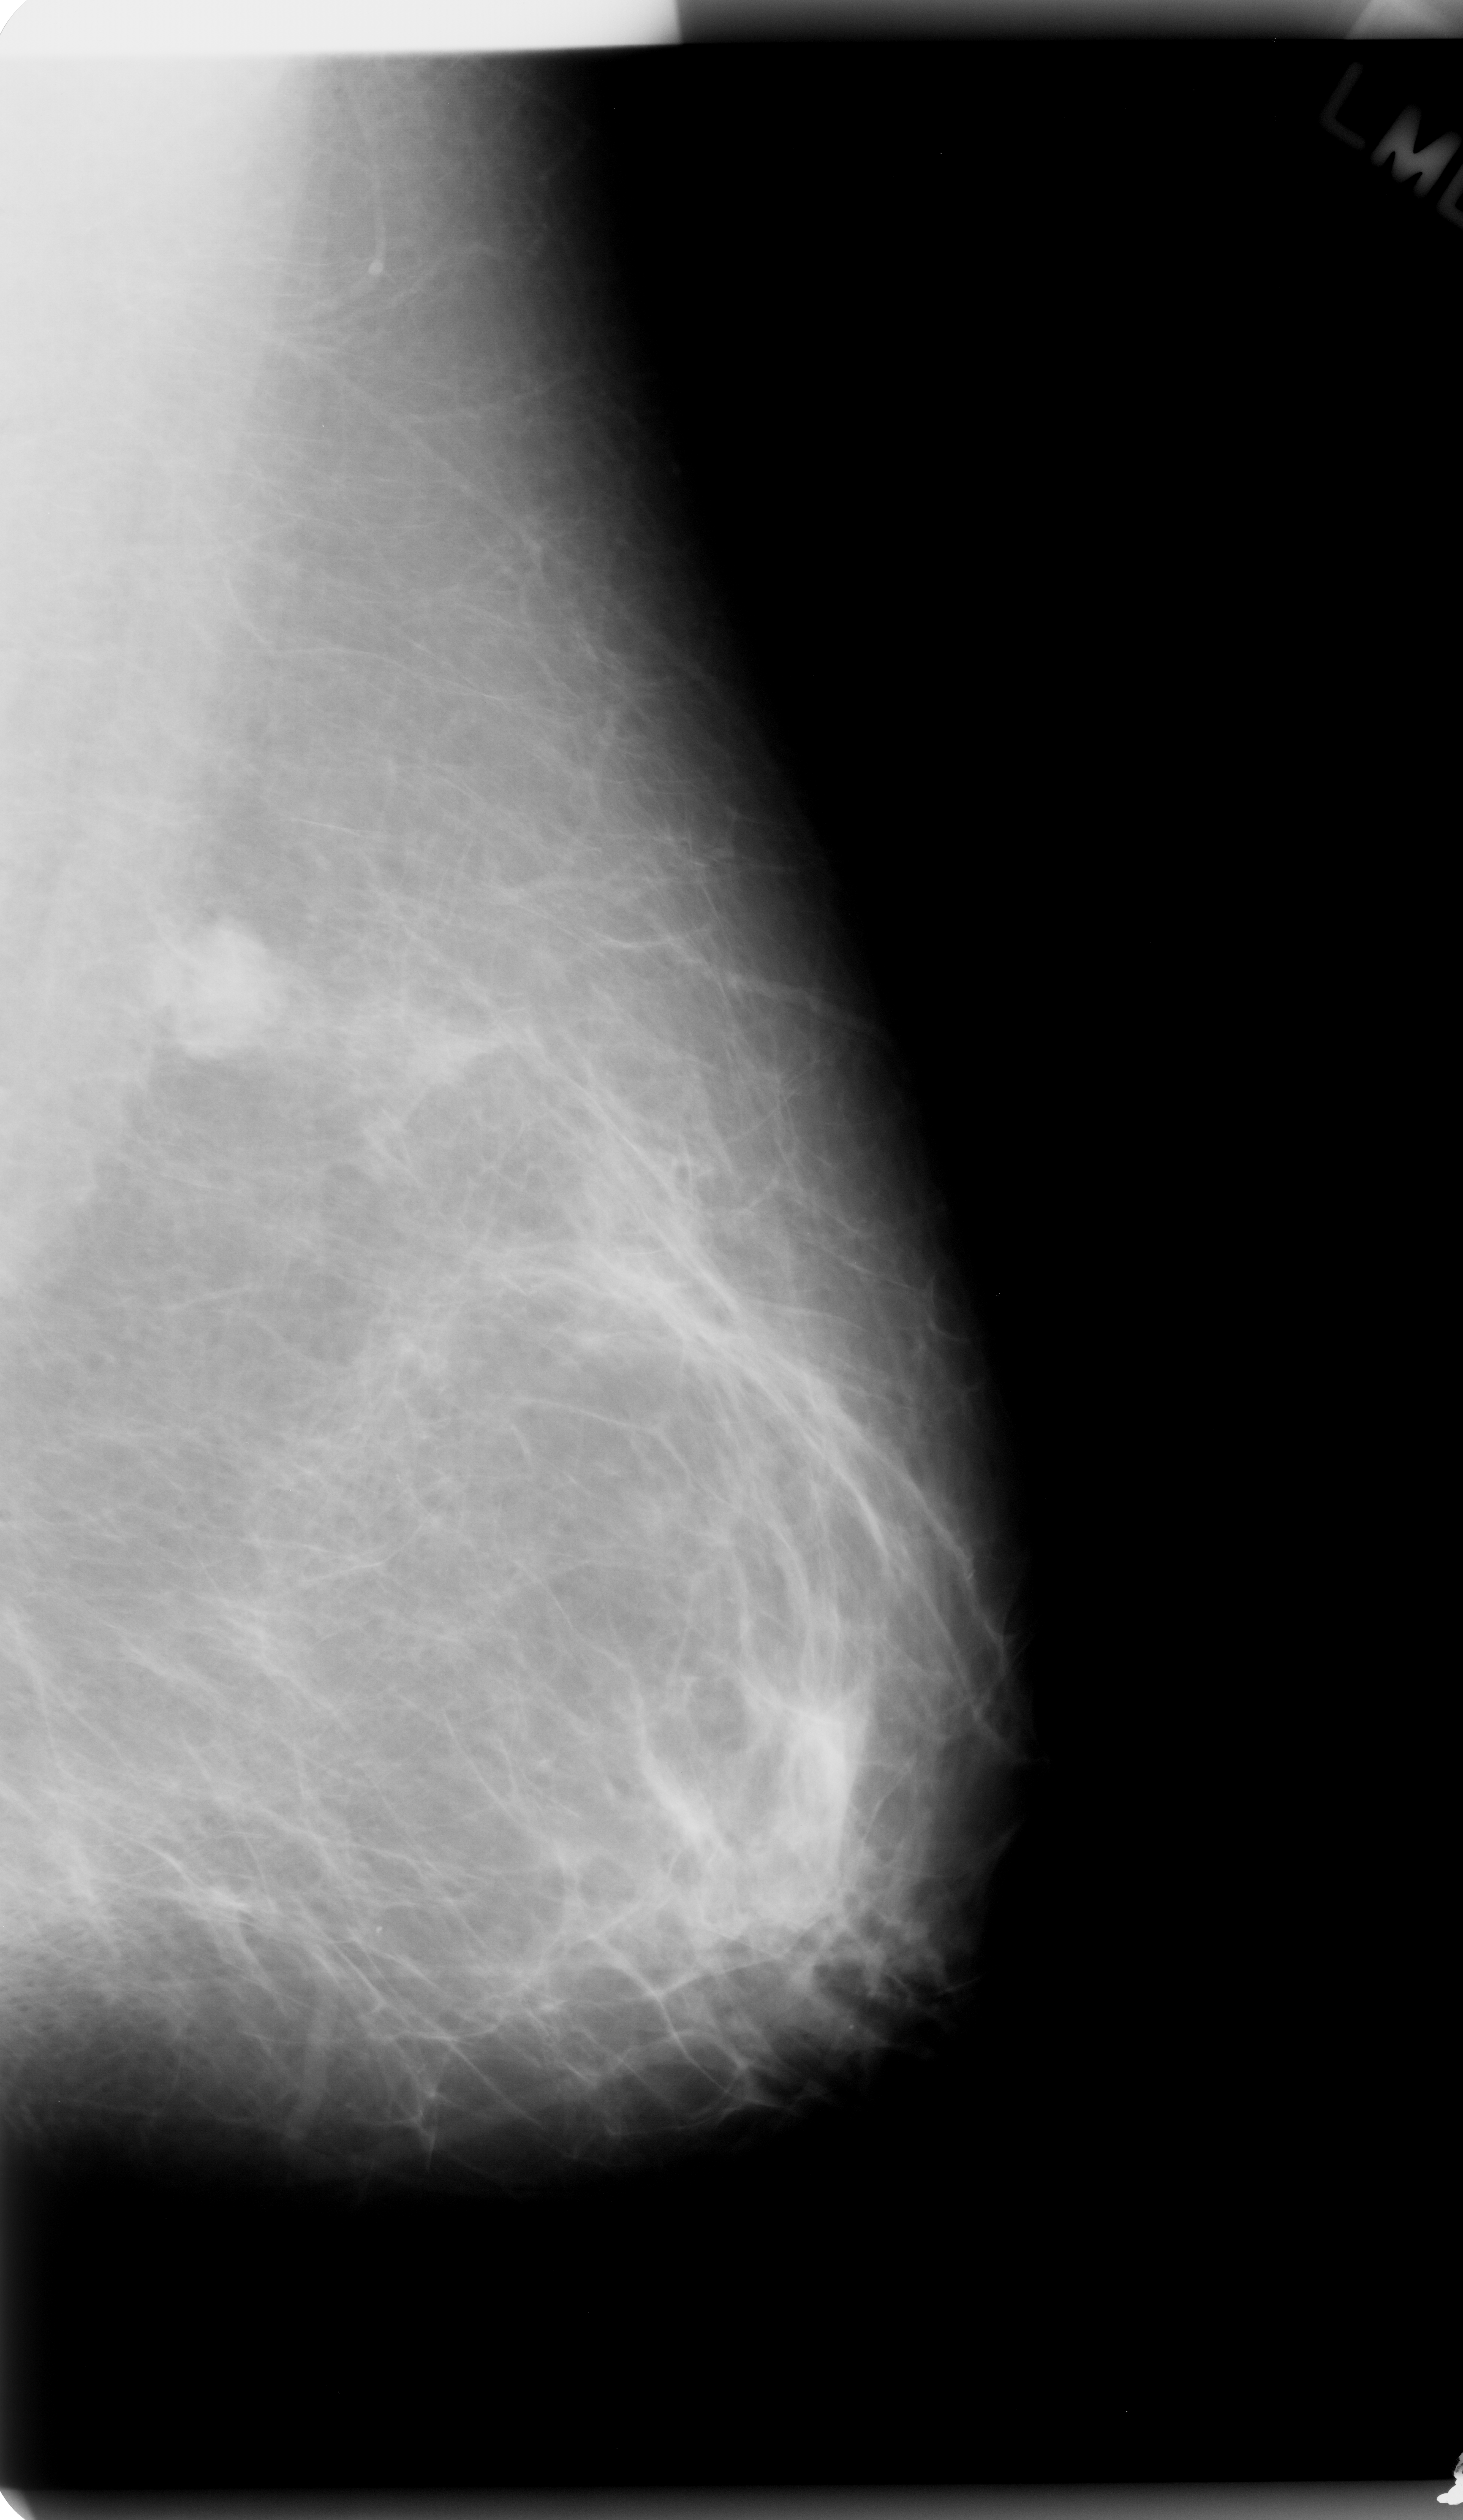
Scanned film-screen mammogram; left breast; mediolateral oblique (MLO) view; breast composition: almost entirely fatty (BI-RADS density category 1 of 4).
Radiologist-marked abnormalities on this image: mass, shape oval, margins microlobulated; BI-RADS assessment category 5; subtlety rating 5 on a 1 (subtle) to 5 (obvious) scale; pathology (as recorded): malignant.